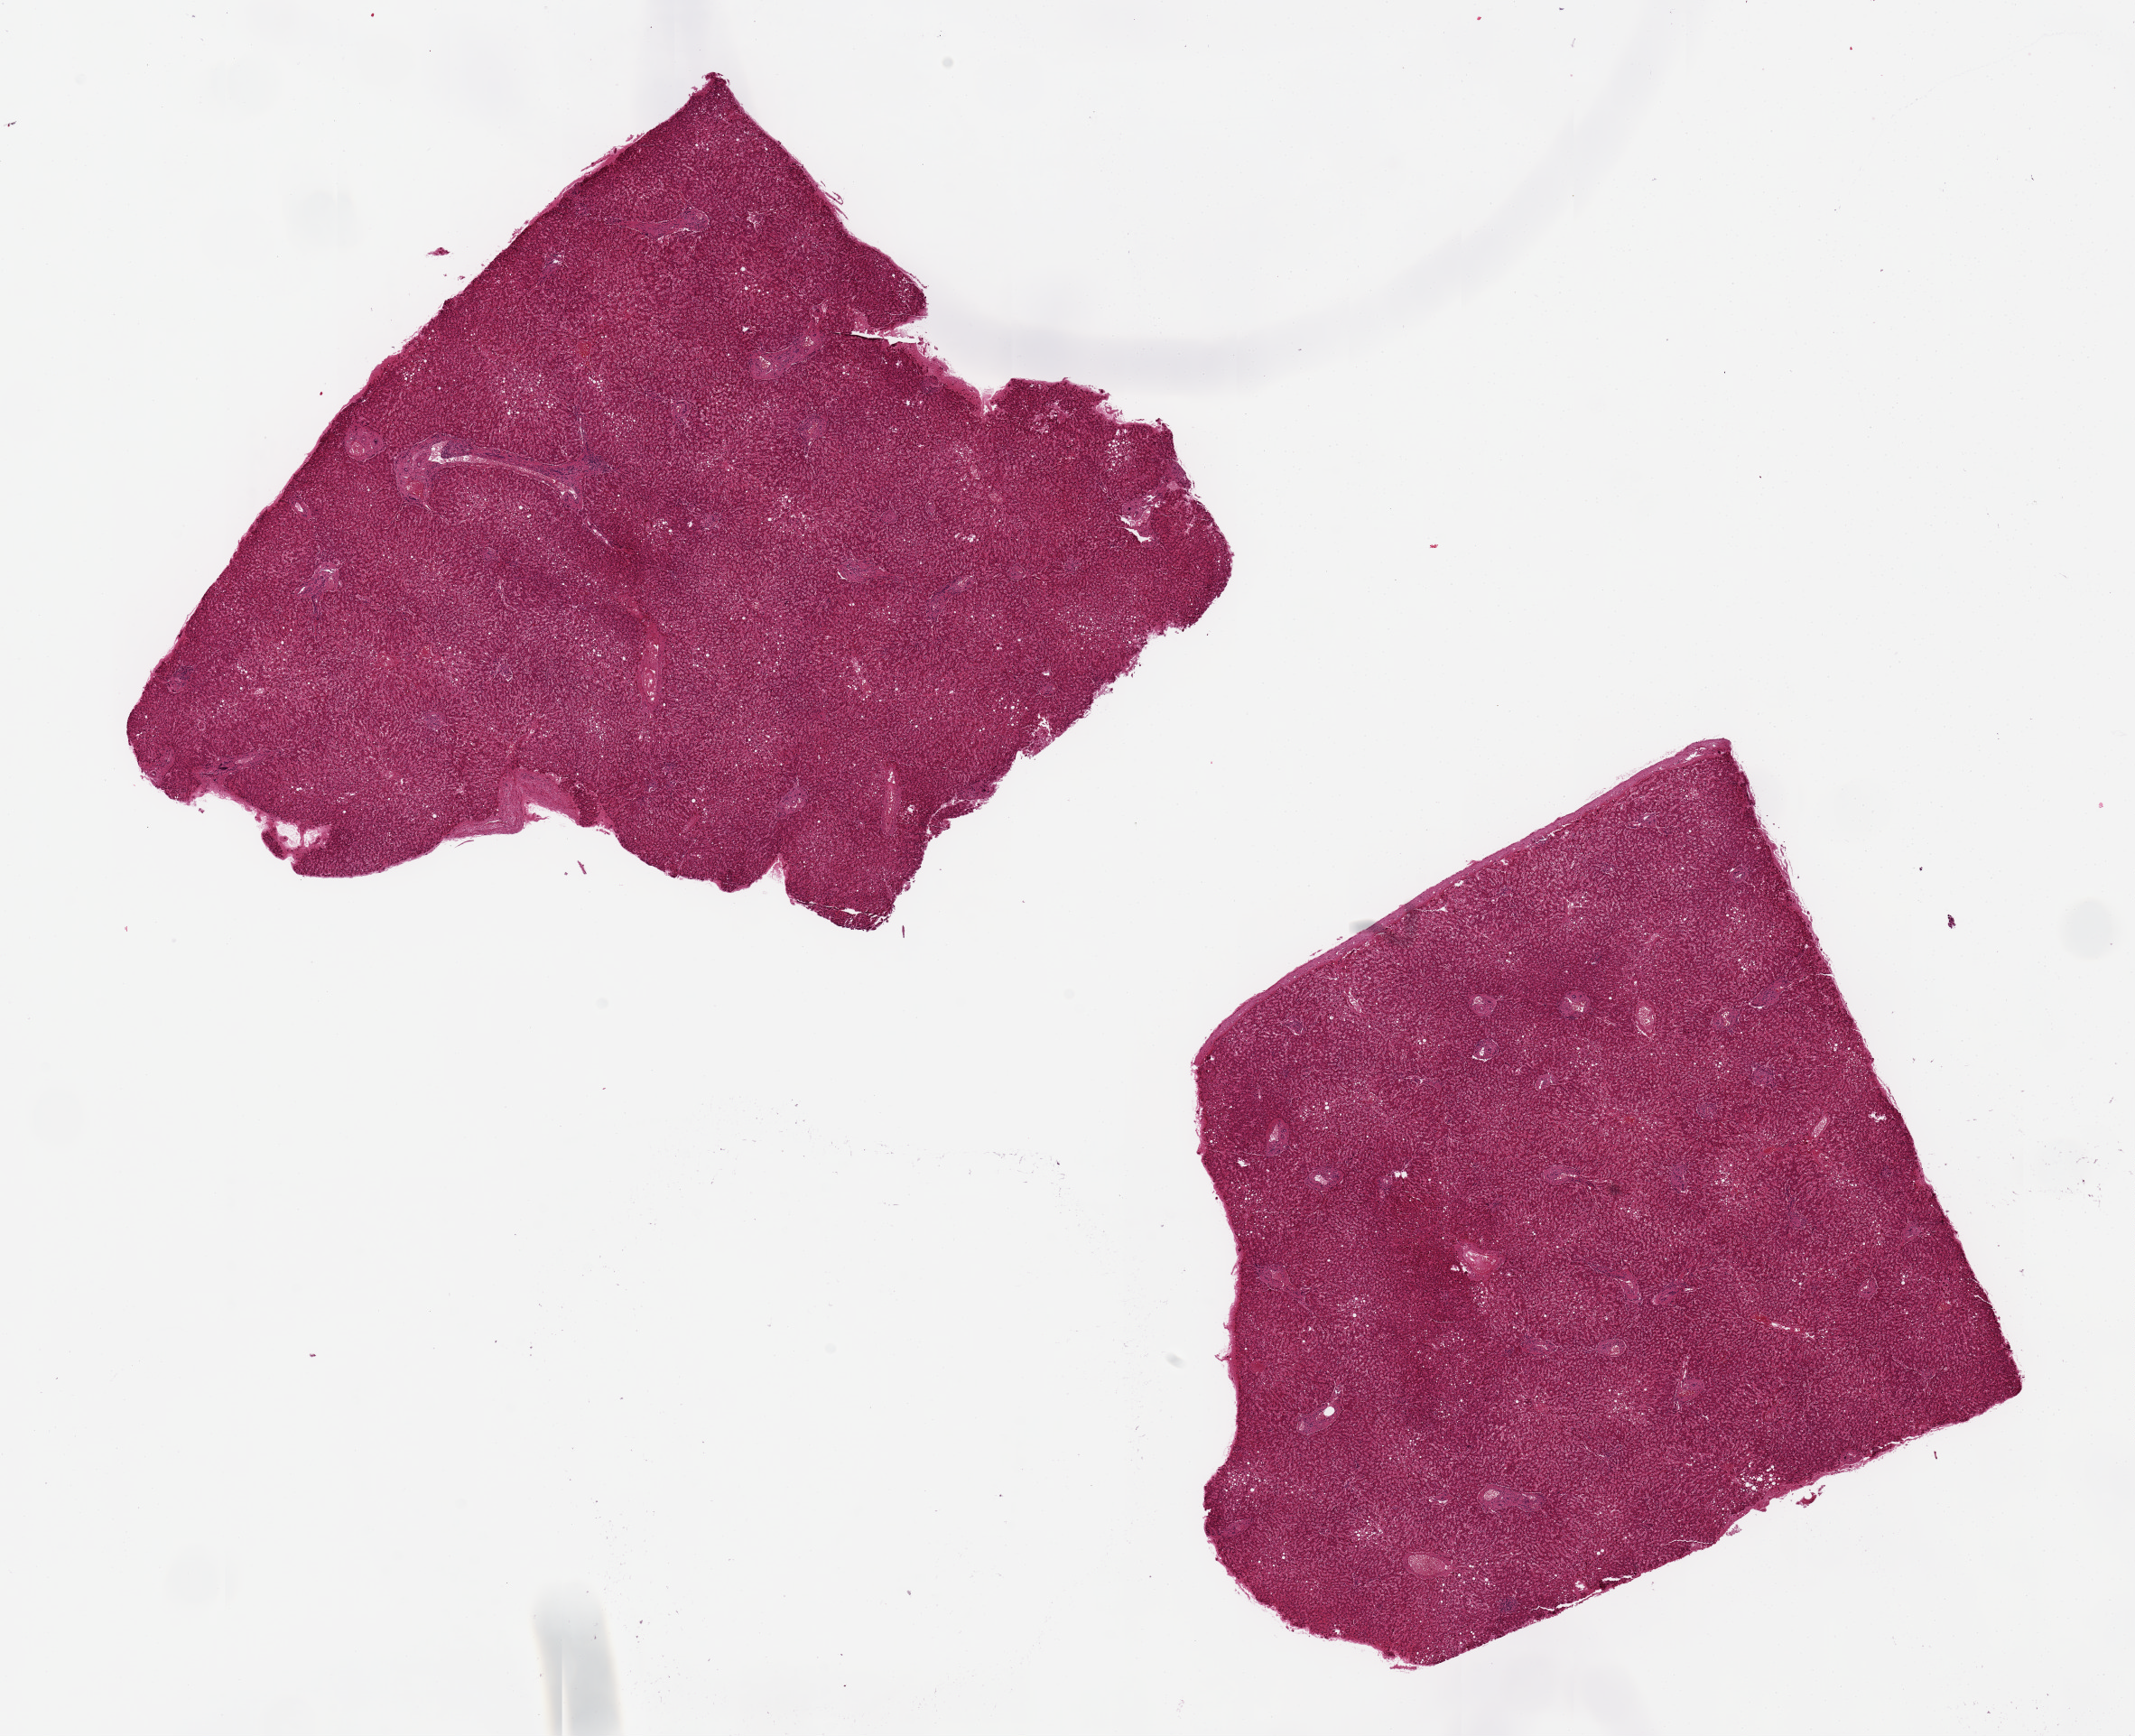
Whole-slide image, H&E stain, shown as a low-resolution overview of the whole scanned area (about 18.7 x 15.2 mm), PAXgene-fixed, paraffin-embedded tissue, section of liver (target tissue), tissue donor sample. Donor: female.
Review note (as recorded): 2 aliquots, ~7x6mm. Moderate congestion, focal microvesicular steatosis involves ~10-15% of parenchyma.